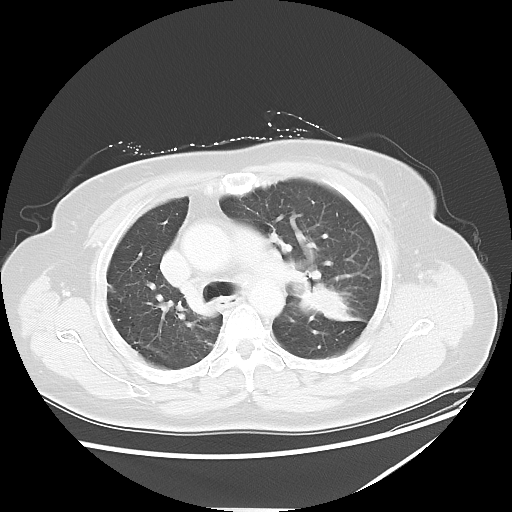
Chest CT, one axial slice. Position 38 of 54 along the scan axis. Reconstruction kernel LUNG. Lung window (W 1500 / L -600 HU). 5 mm slice thickness. 512 × 512 image matrix, field of view 384 × 384 mm. Patient: female, 61 years. Case-level facts recorded for this patient, not image findings: clinical TNM (as recorded): T1c N3 M1.
Outlined on this slice (rectangle marked by the reading radiologist):
- lung tumour (recorded histology: adenocarcinoma): box from (x=299, y=281) to (x=366, y=324) px